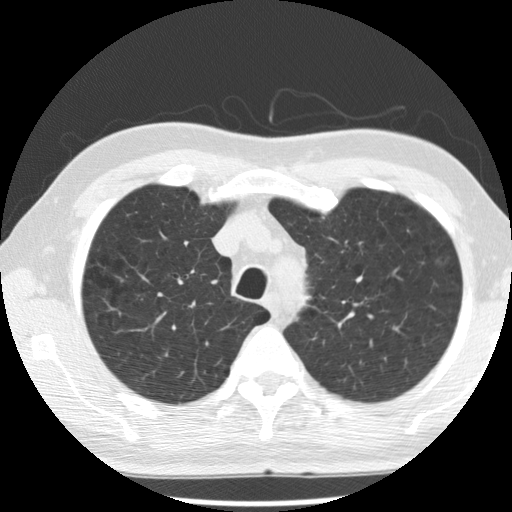
Chest CT (low-dose screening protocol), one axial image. Baseline annual screen. Lung window (W 1500 / L -600 HU). 2.5 mm slice thickness. Standard (soft-tissue) reconstruction kernel (STANDARD). Slice 59 of 277 in the series. Male participant, aged 68 years at enrolment. Current smoker at enrolment.
Expert reader's lesion annotation, bounding box (x1, y1, x2, y2) in pixels: (429, 248, 464, 280). The exam's reader record, not a measurement of the box and not confirmed to be the same lesion: non-calcified nodule or mass ≥4 mm, left upper lobe, 5 × 5 mm, poorly defined margins, ground glass attenuation. Official screen result: positive, change unspecified: nodule(s) >= 4 mm or enlarging nodule(s), mass(es), or other non-specific abnormalities suspicious for lung cancer. Participant outcome: lung cancer diagnosed 648 days after this screen — bronchiolo-alveolar adenocarcinoma, NOS, left upper lobe, moderately differentiated (G2), stage IA (AJCC 6th edition), 17 mm at pathology.